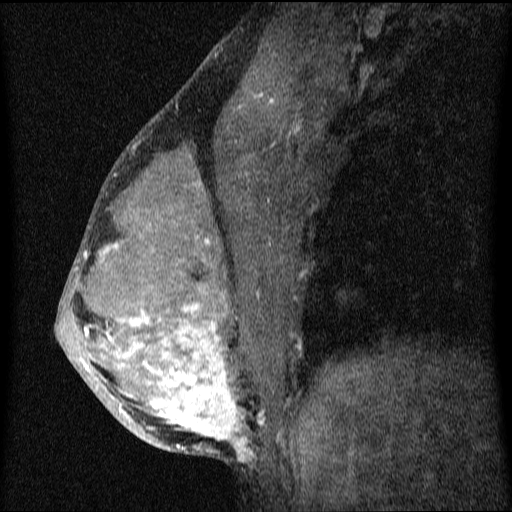
Breast MRI (dynamic contrast-enhanced), one sagittal slice. Position 36 of 64 along the scan axis. Dynamic contrast-enhanced series, image 2 of 4 at this slice position (ordered by acquisition). 1.5 T. TE 4.2 ms, TR 9.1 ms. 512 × 512 image matrix. Female patient, age 33 years.
Outlined on this slice (semi-automatically segmented with operator editing):
- analysis volume of interest (the breast-tissue region the enhancement analysis was run in; not a lesion): box from (x=57, y=151) to (x=336, y=458) px
- tumour enhancement mask (voxels above the 70 % enhancement threshold inside the analysis volume of interest): (x=70, y=239)–(x=254, y=458)